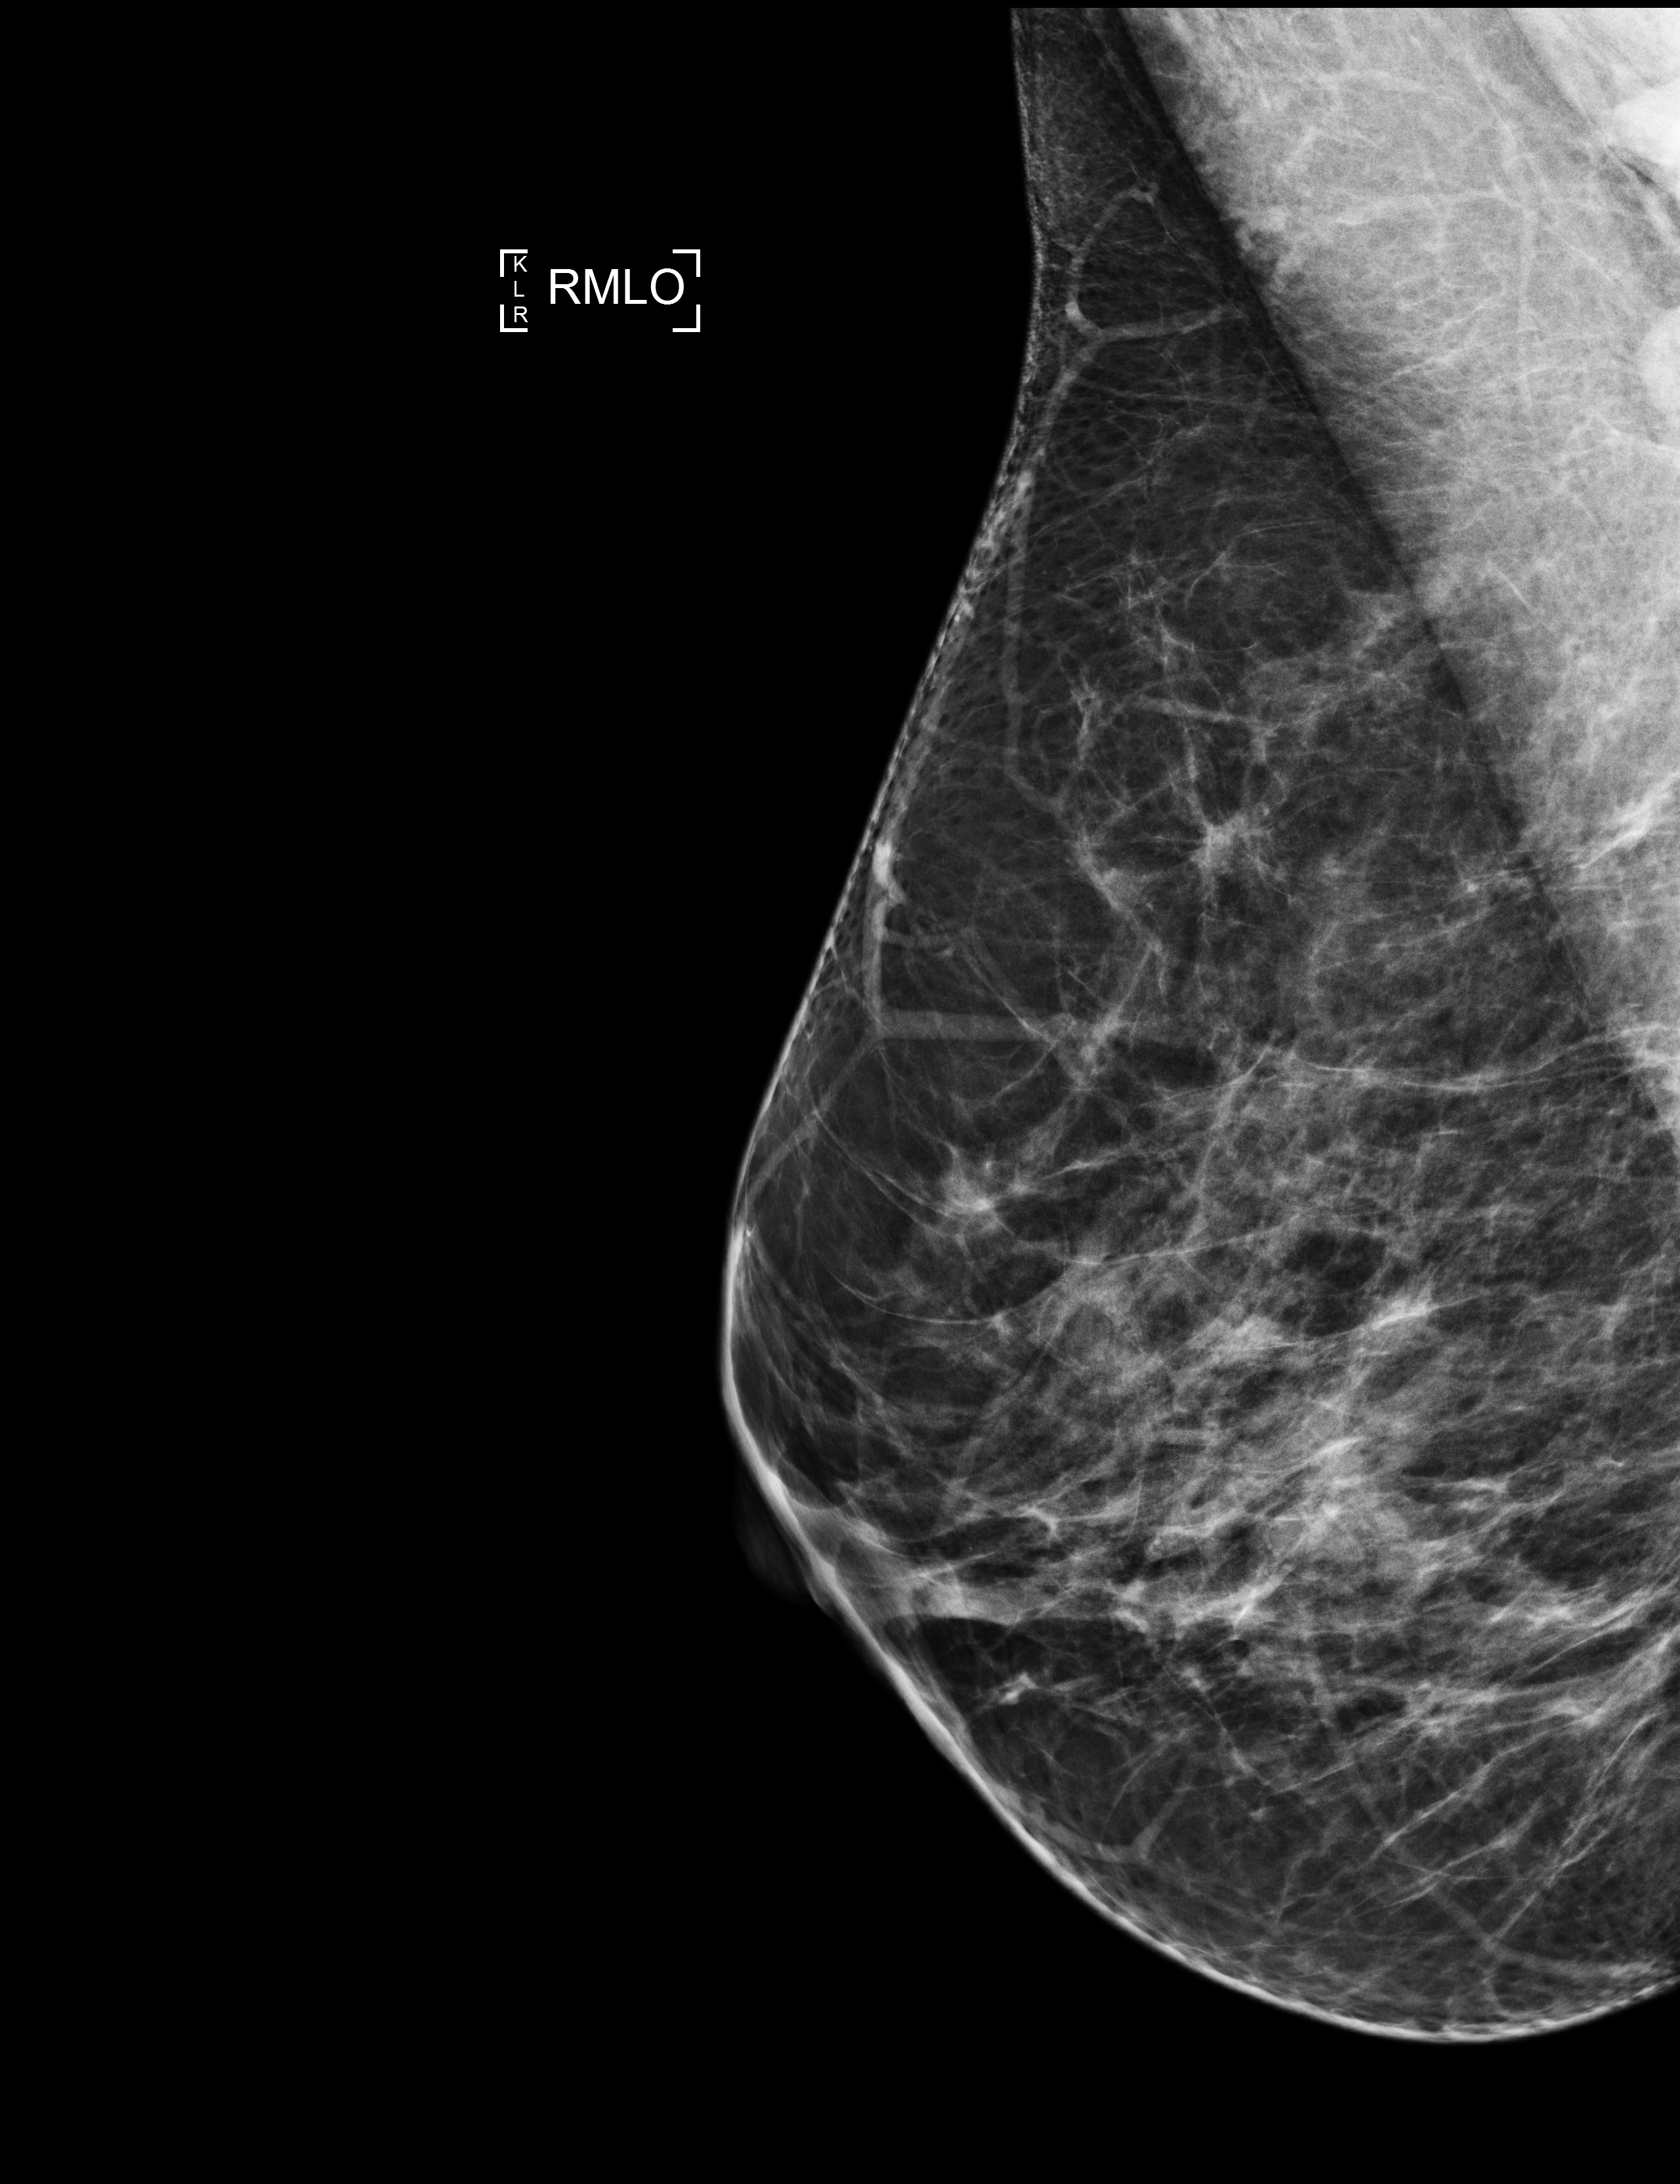
Full-field digital mammogram (FFDM); right breast; medio-lateral oblique projection; annual screening mammography examination. Patient: female, 47 years.
BI-RADS breast density category at the screening exam (both breasts, scale 1–4): 2. Final BI-RADS category for the screening round (tomosynthesis exam, both breasts): category 1. Recall: no recall after this screen.